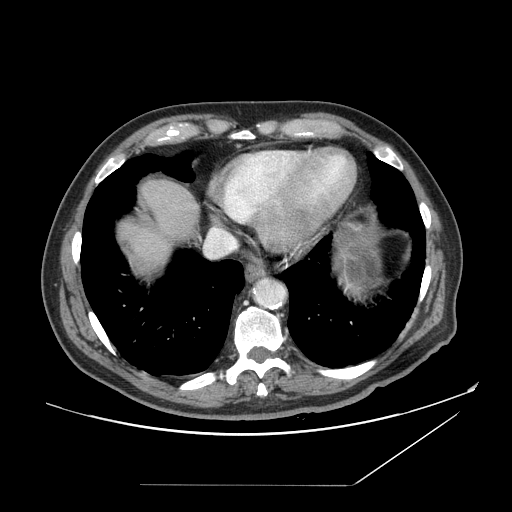
Contrast-enhanced abdominal CT, one axial slice. Position 142 of 166 along the scan axis. 120 kVp. Soft-tissue window (W 400 / L 40 HU). 2.5 mm slice thickness. 512 × 512 image matrix, field of view 416 × 416 mm. Male patient, age 80 years. From the clinical record (not read from this slice): diagnosis: colorectal cancer liver metastases, imaged before liver resection; multiple liver metastases: no; largest metastasis: 2.2 cm; chemotherapy before resection: no.
Outlined on this slice (expert manual segmentation):
- liver: bounding box (x1, y1, x2, y2) in pixels: (116, 180, 200, 283)
- planned liver remnant (the part of the liver to remain after resection): (116, 180, 199, 257)